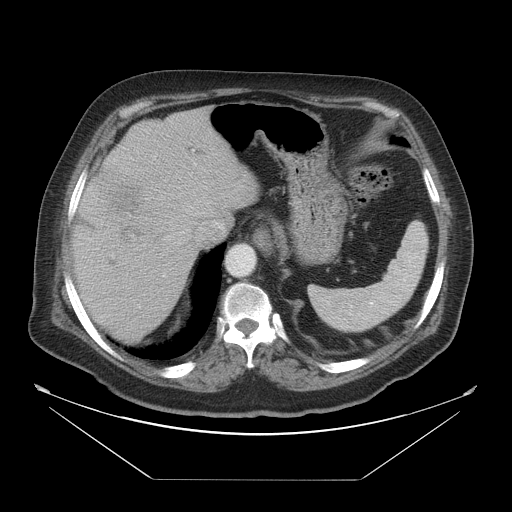
Contrast-enhanced abdominal CT, one axial slice. Position 39 of 45 along the scan axis. Reconstruction kernel STANDARD. Intravenous contrast given. Soft-tissue window (W 400 / L 40 HU). 5 mm slice thickness. 512 × 512 image matrix, field of view 463 × 463 mm. Male patient, age 87 years. From the clinical record (not read from this slice): diagnosis: colorectal cancer liver metastases, imaged before liver resection.
Outlined on this slice (outlined manually by an expert reader):
- hepatic veins: box from (x=164, y=206) to (x=205, y=240) px
- liver: (x=72, y=106)–(x=260, y=342)
- planned liver remnant (the part of the liver to remain after resection): (x=111, y=106)–(x=260, y=214)
- portal vein (with intrahepatic branches): (x=131, y=150)–(x=194, y=241)
- liver metastasis: (x=114, y=221)–(x=149, y=245)
- liver metastasis: (x=95, y=165)–(x=148, y=218)